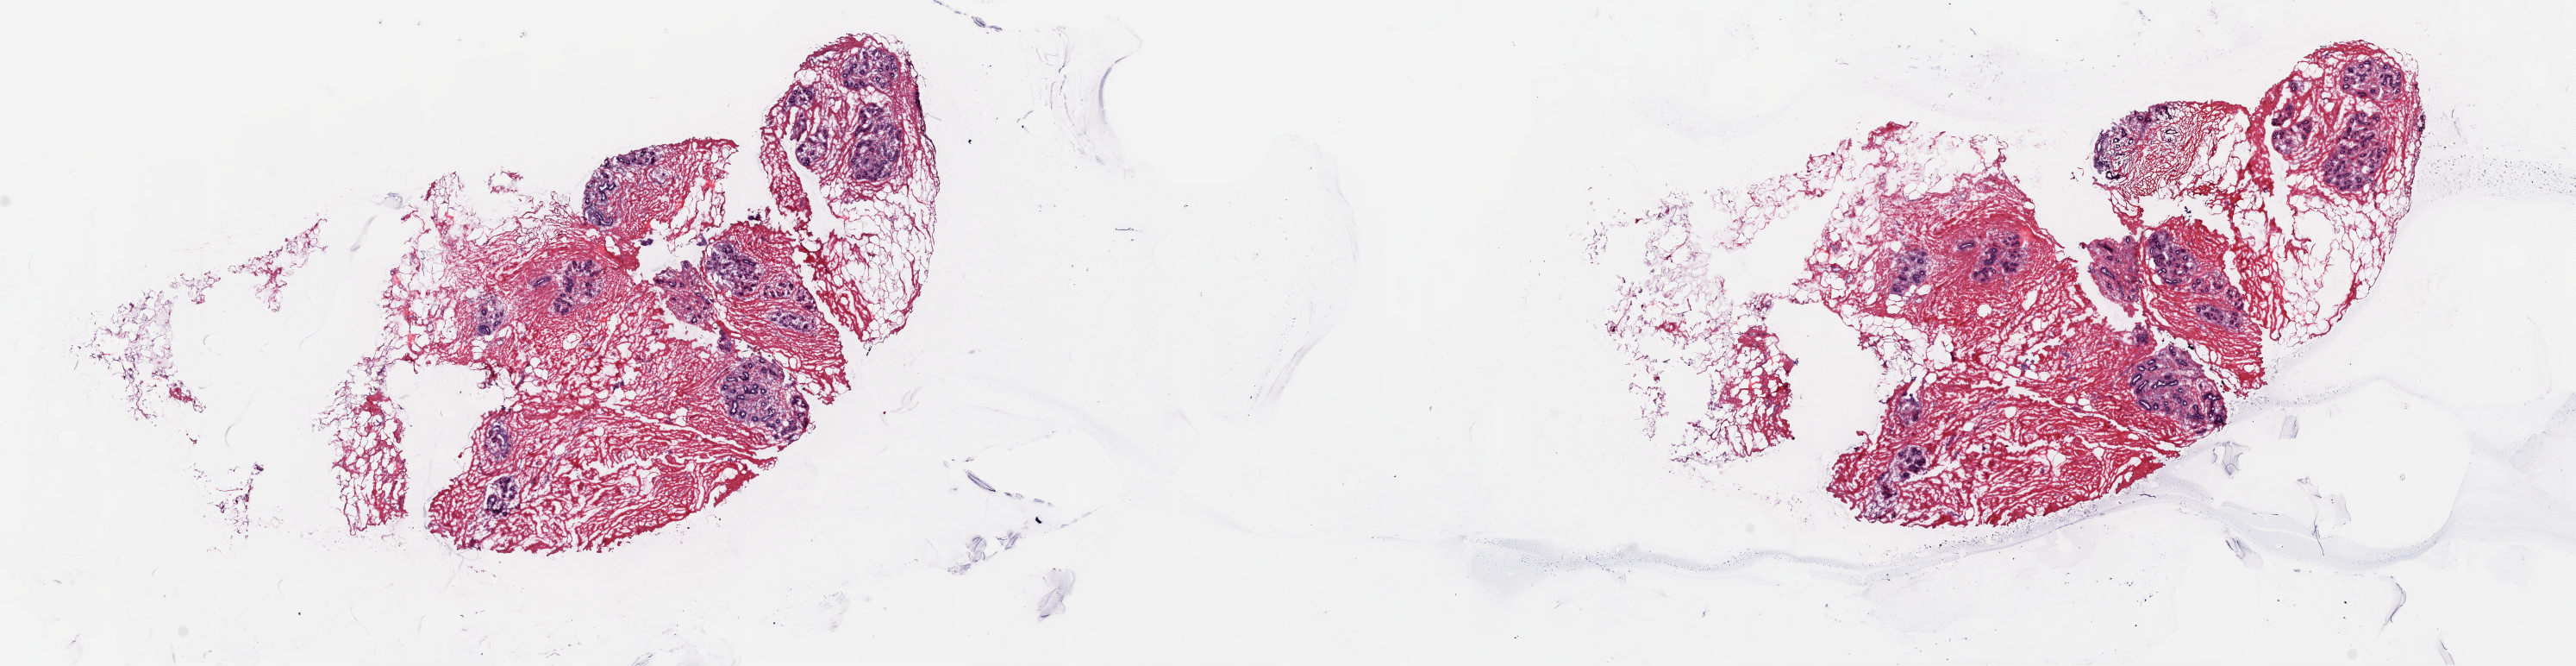
Digitized H&E-stained tissue section (whole slide) — shown as a low-resolution overview of the whole scanned area (about 23.7 x 6.1 mm, acquisition: 20x scan); frozen section from the top of the tissue portion; sample: solid tissue normal (non-tumour tissue), breast. Patient: female, age at initial diagnosis 41 years. Pathologist review of this section (percent, as recorded): tumour cells 0%, tumour nuclei 0%, normal cells 100%, stromal cells 0%, necrosis 0%. Infiltration values recorded for this section: lymphocyte infiltration 0%, monocyte infiltration 0%, neutrophil infiltration 0%.
This section: solid tissue normal (non-tumour) sample from the same patient. Patient diagnosis: Infiltrating duct carcinoma, NOS.